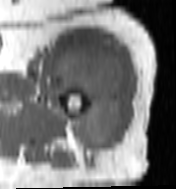
MRI of an extremity soft-tissue mass, one axial slice; position 81 of 100 along the scan axis; MR volume resampled by the dataset authors to the PET/CT grid (not the native acquisition matrix); 3.27 mm slice thickness; 176 × 189 image matrix, field of view 172 × 185 mm. Female patient. Case-level facts recorded for this patient, not image findings: histological type: undifferentiated – high grade; grade: high; site of the primary tumour: left thigh.
Outlined on this slice (expert contour drawn on MRI and transferred to this co-registered scan by the dataset authors):
- gross tumour volume including surrounding oedema: box from (x=53, y=45) to (x=124, y=151) px
- gross tumour volume (mass): (x=55, y=50)–(x=122, y=151)